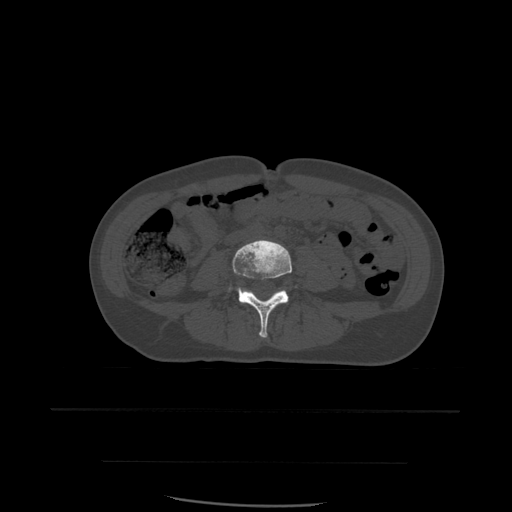
CT including the spine, one axial slice. Slice 170 of 574 in the series (ordered by position). Bone window (W 1800 / L 400 HU). 512 × 512 image matrix, field of view 392 × 392 mm. Patient age 48 years. Case-level facts recorded for this patient, not image findings: primary cancer: lung; vertebrae with lytic lesions (as recorded): T11.
Annotated regions visible in this slice (semi-automatically segmented with operator editing):
- L4 vertebra: bounding box <224,240,298,338> (left, top, right, bottom; pixels)